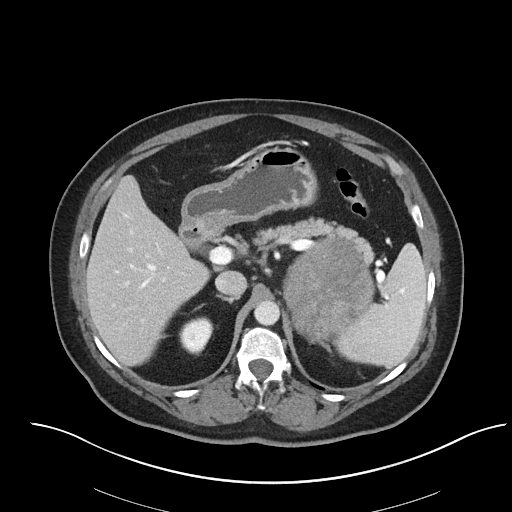
Contrast-enhanced abdominal CT, one axial slice. Position 53 of 92 along the scan axis. Reconstruction kernel I40f/2. 120 kVp. Intravenous contrast given. Soft-tissue window (W 400 / L 40 HU). 3 mm slice thickness. 512 × 512 image matrix. Patient: female, 53 years. From the clinical record (not read from this slice): diagnosis: adrenocortical carcinoma; tumour side: left adrenal; tumour size at pathology: 9 cm; Ki-67 index: 28 %; stage (as recorded): 2.
Outlined on this slice (semi-automatic segmentation, software-assisted and operator-edited):
- mass: box from (x=284, y=240) to (x=373, y=339) px